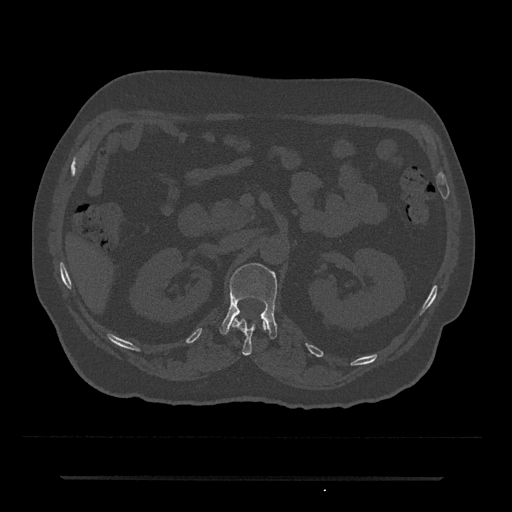
CT including the spine, one axial slice; position 91 of 797 along the scan axis; reconstruction kernel Br40s/3; bone window (W 1800 / L 400 HU); 0.5 mm slice thickness; 512 × 512 image matrix, field of view 437 × 437 mm. Male patient, age 69 years. From the clinical record (not read from this slice): primary cancer: prostate.
Outlined on this slice (semi-automatically segmented with operator editing):
- L1 vertebra: box from (x=219, y=263) to (x=277, y=339) px
- T12 vertebra: (x=231, y=315)–(x=267, y=356)